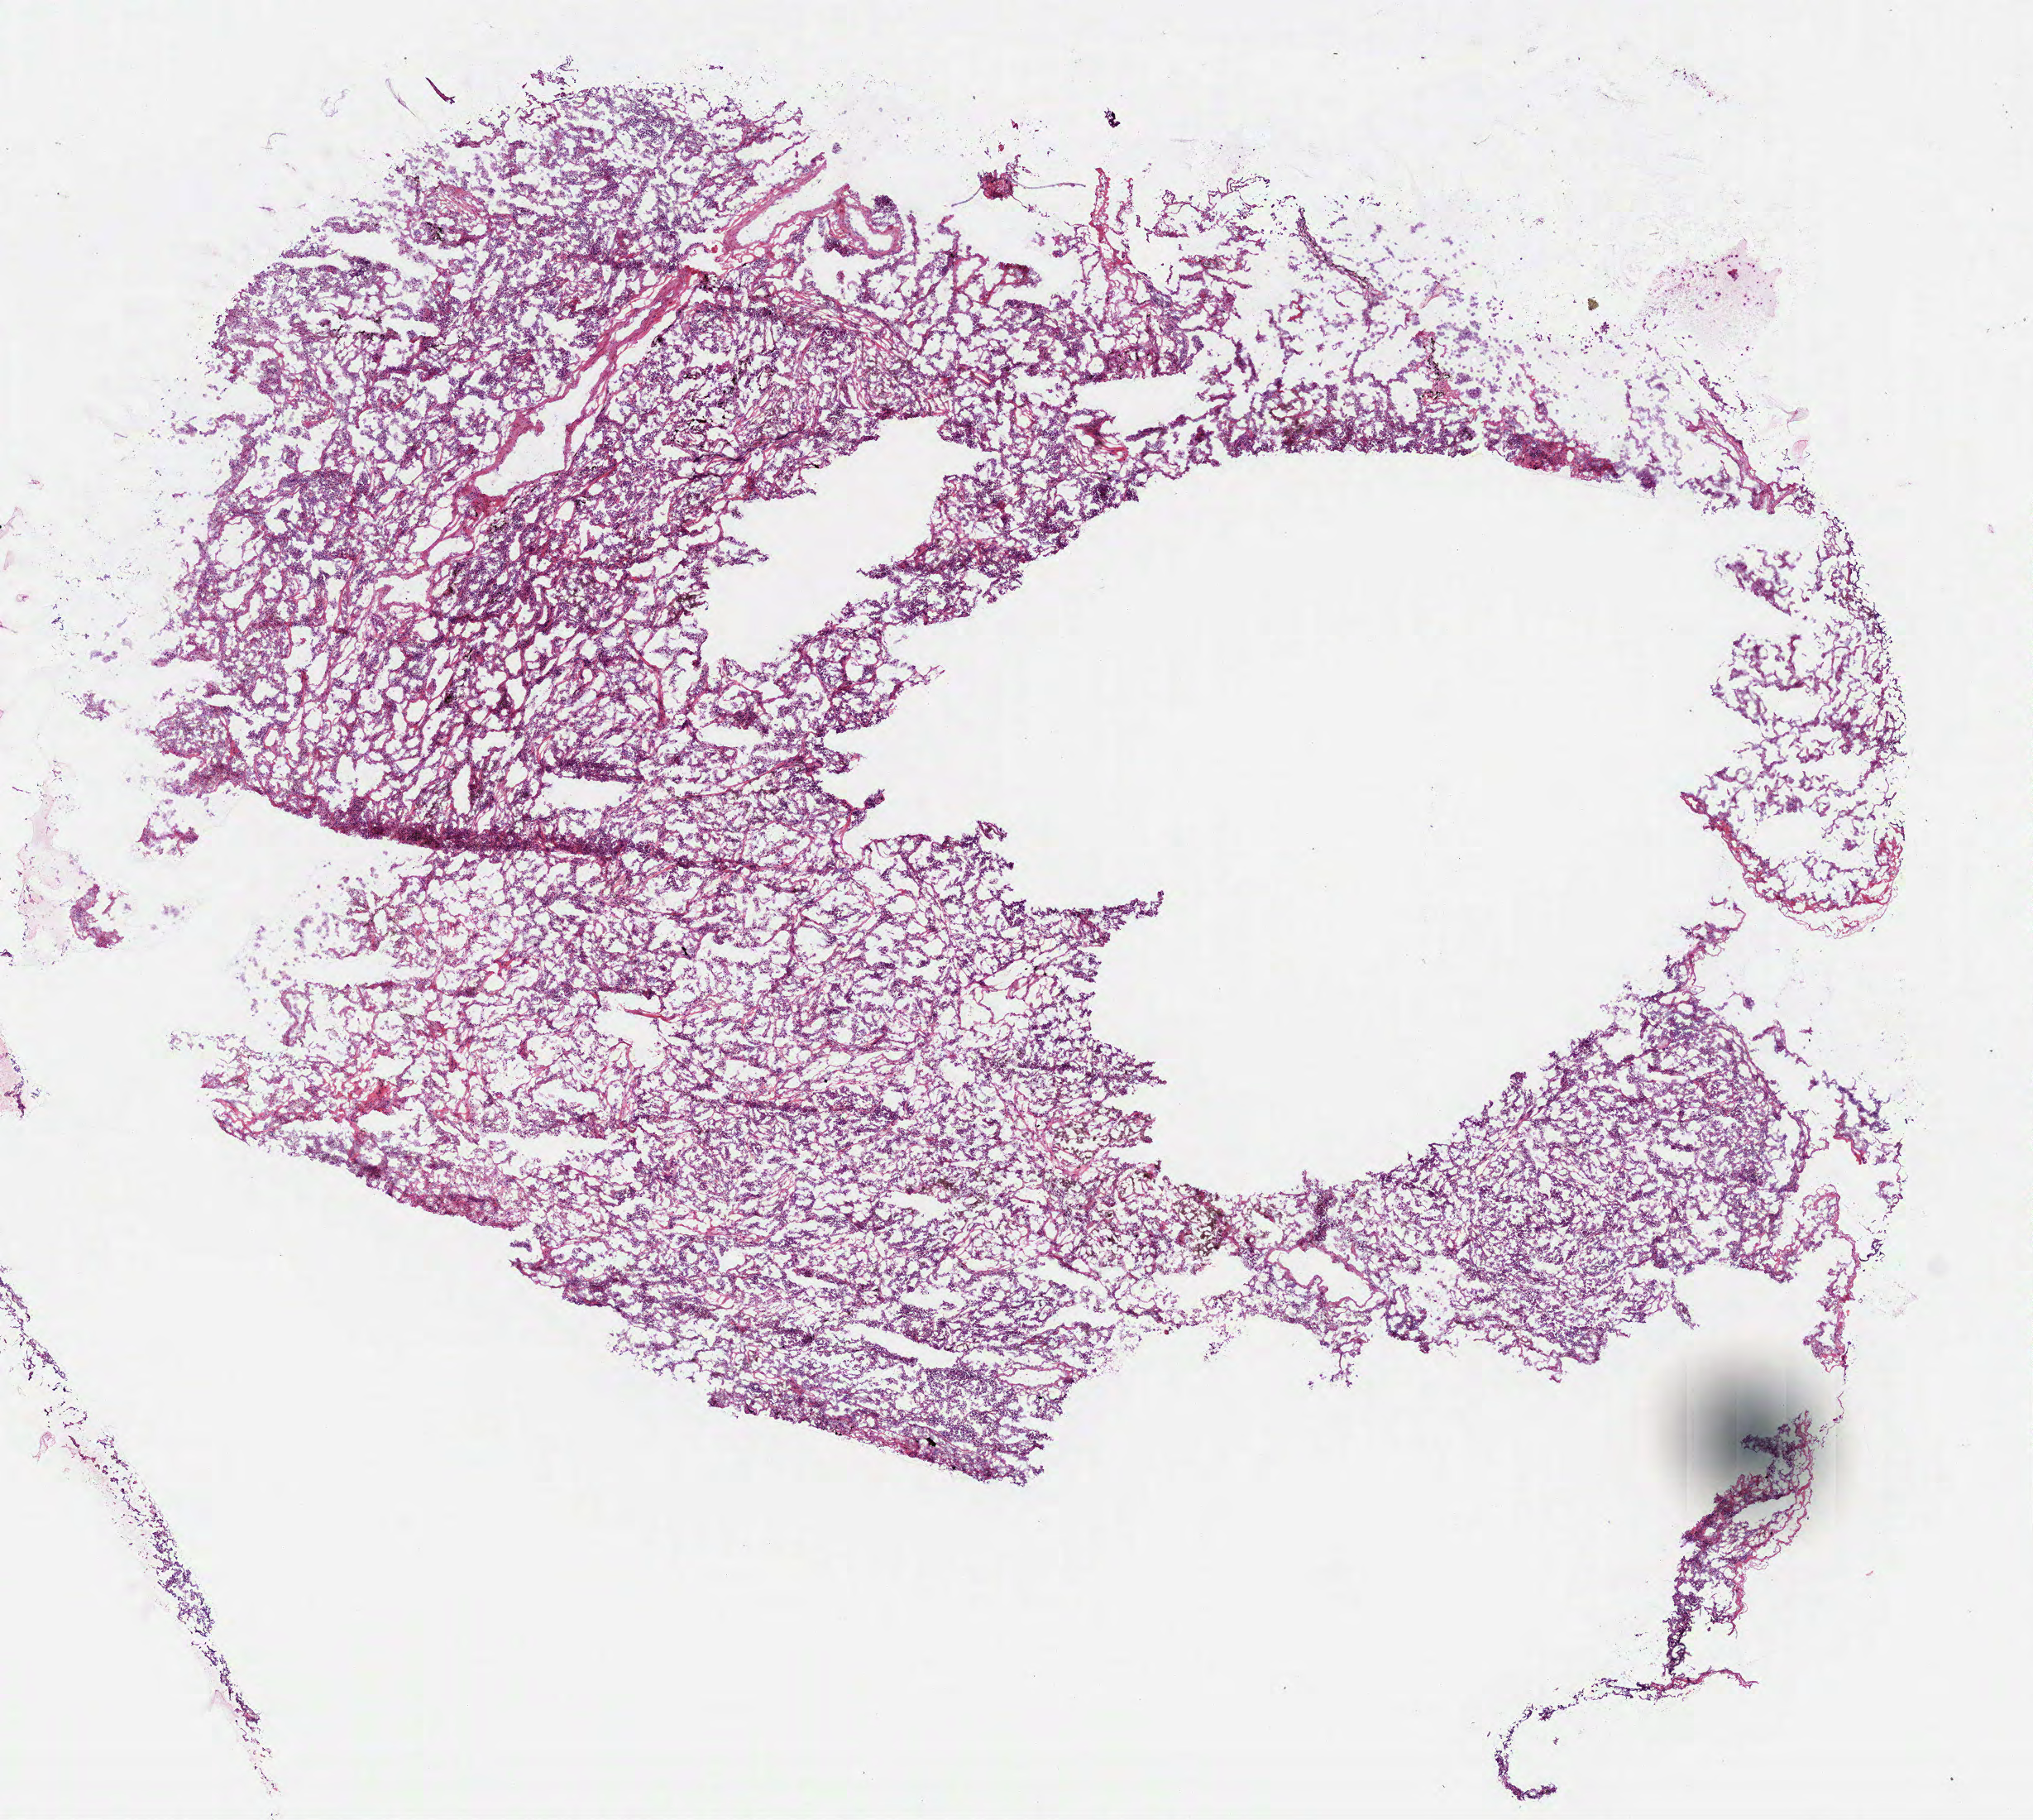
H&E whole-slide image — shown as a low-resolution overview of the whole scanned area (about 9.9 x 8.9 mm, slide scanned at 40x). Frozen section from the bottom of the tissue portion. Lung, primary tumour sample. Male, age 60 years at initial diagnosis. Slide review estimates, as recorded: tumour cells 80%, tumour nuclei 55%, normal cells 5%, stromal cells 10%, necrosis 5%. Inflammatory infiltration, as recorded: lymphocyte infiltration 1%, monocyte infiltration 15%, neutrophil infiltration 0%.
* pathologic diagnosis: Adenocarcinoma, NOS (lower lobe, lung)
* AJCC pathologic stage: IA (7th edition)